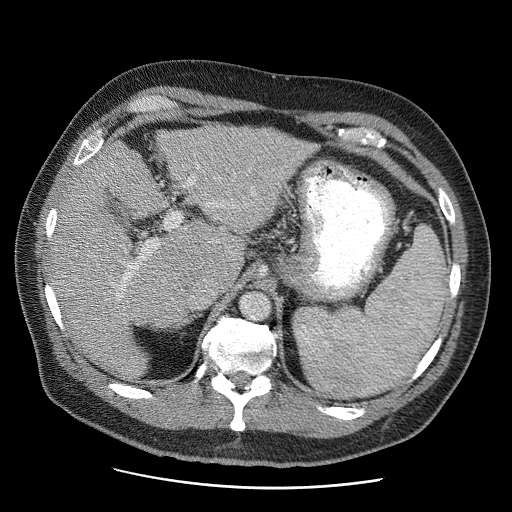
Contrast-enhanced abdominal CT (liver protocol), one axial slice. Slice 35 of 81 in the series (ordered by position). Reconstruction kernel STANDARD. Soft-tissue window (W 400 / L 40 HU). 2.5 mm slice thickness. 512 × 512 image matrix. From the clinical record (not read from this slice): diagnosis: hepatocellular carcinoma (patient treated with transarterial chemoembolisation; whether this scan precedes or follows treatment is not stated here); TNM stage (as recorded): Stage-IIIA; Child-Pugh class: A; tumour differentiation: moderately differentiated; tumour size: 5.5 cm.
Structures marked on this image (semi-automatic segmentation, software-assisted and operator-edited):
- liver parenchyma outside the tumour (the mass and vessels are separate outlines, so this box may not span the whole liver): bounding box [x1, y1, x2, y2] px = [50, 124, 316, 378]
- liver vessels: [121, 166, 217, 290]